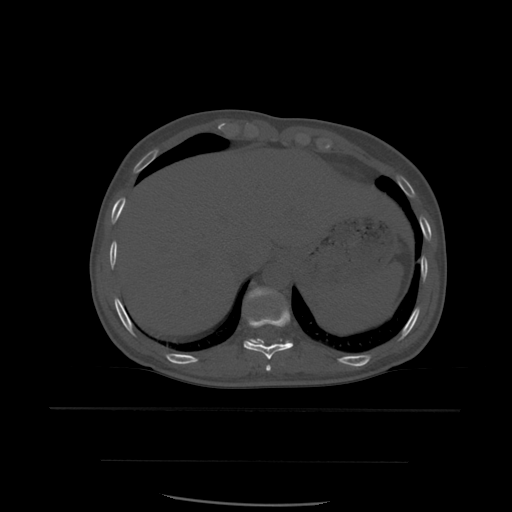
CT including the spine, one axial slice; slice 311 of 574 in the series (ordered by position); bone window (W 1800 / L 400 HU); 1.25 mm slice thickness; 512 × 512 image matrix, field of view 392 × 392 mm. Patient age 48 years. From the clinical record (not read from this slice): primary cancer: lung.
Structures marked on this image (semi-automatic segmentation, software-assisted and operator-edited):
- T10 vertebra: bounding box [x1, y1, x2, y2] px = [244, 304, 294, 360]
- T11 vertebra: [248, 288, 291, 346]
- T9 vertebra: [266, 365, 272, 372]